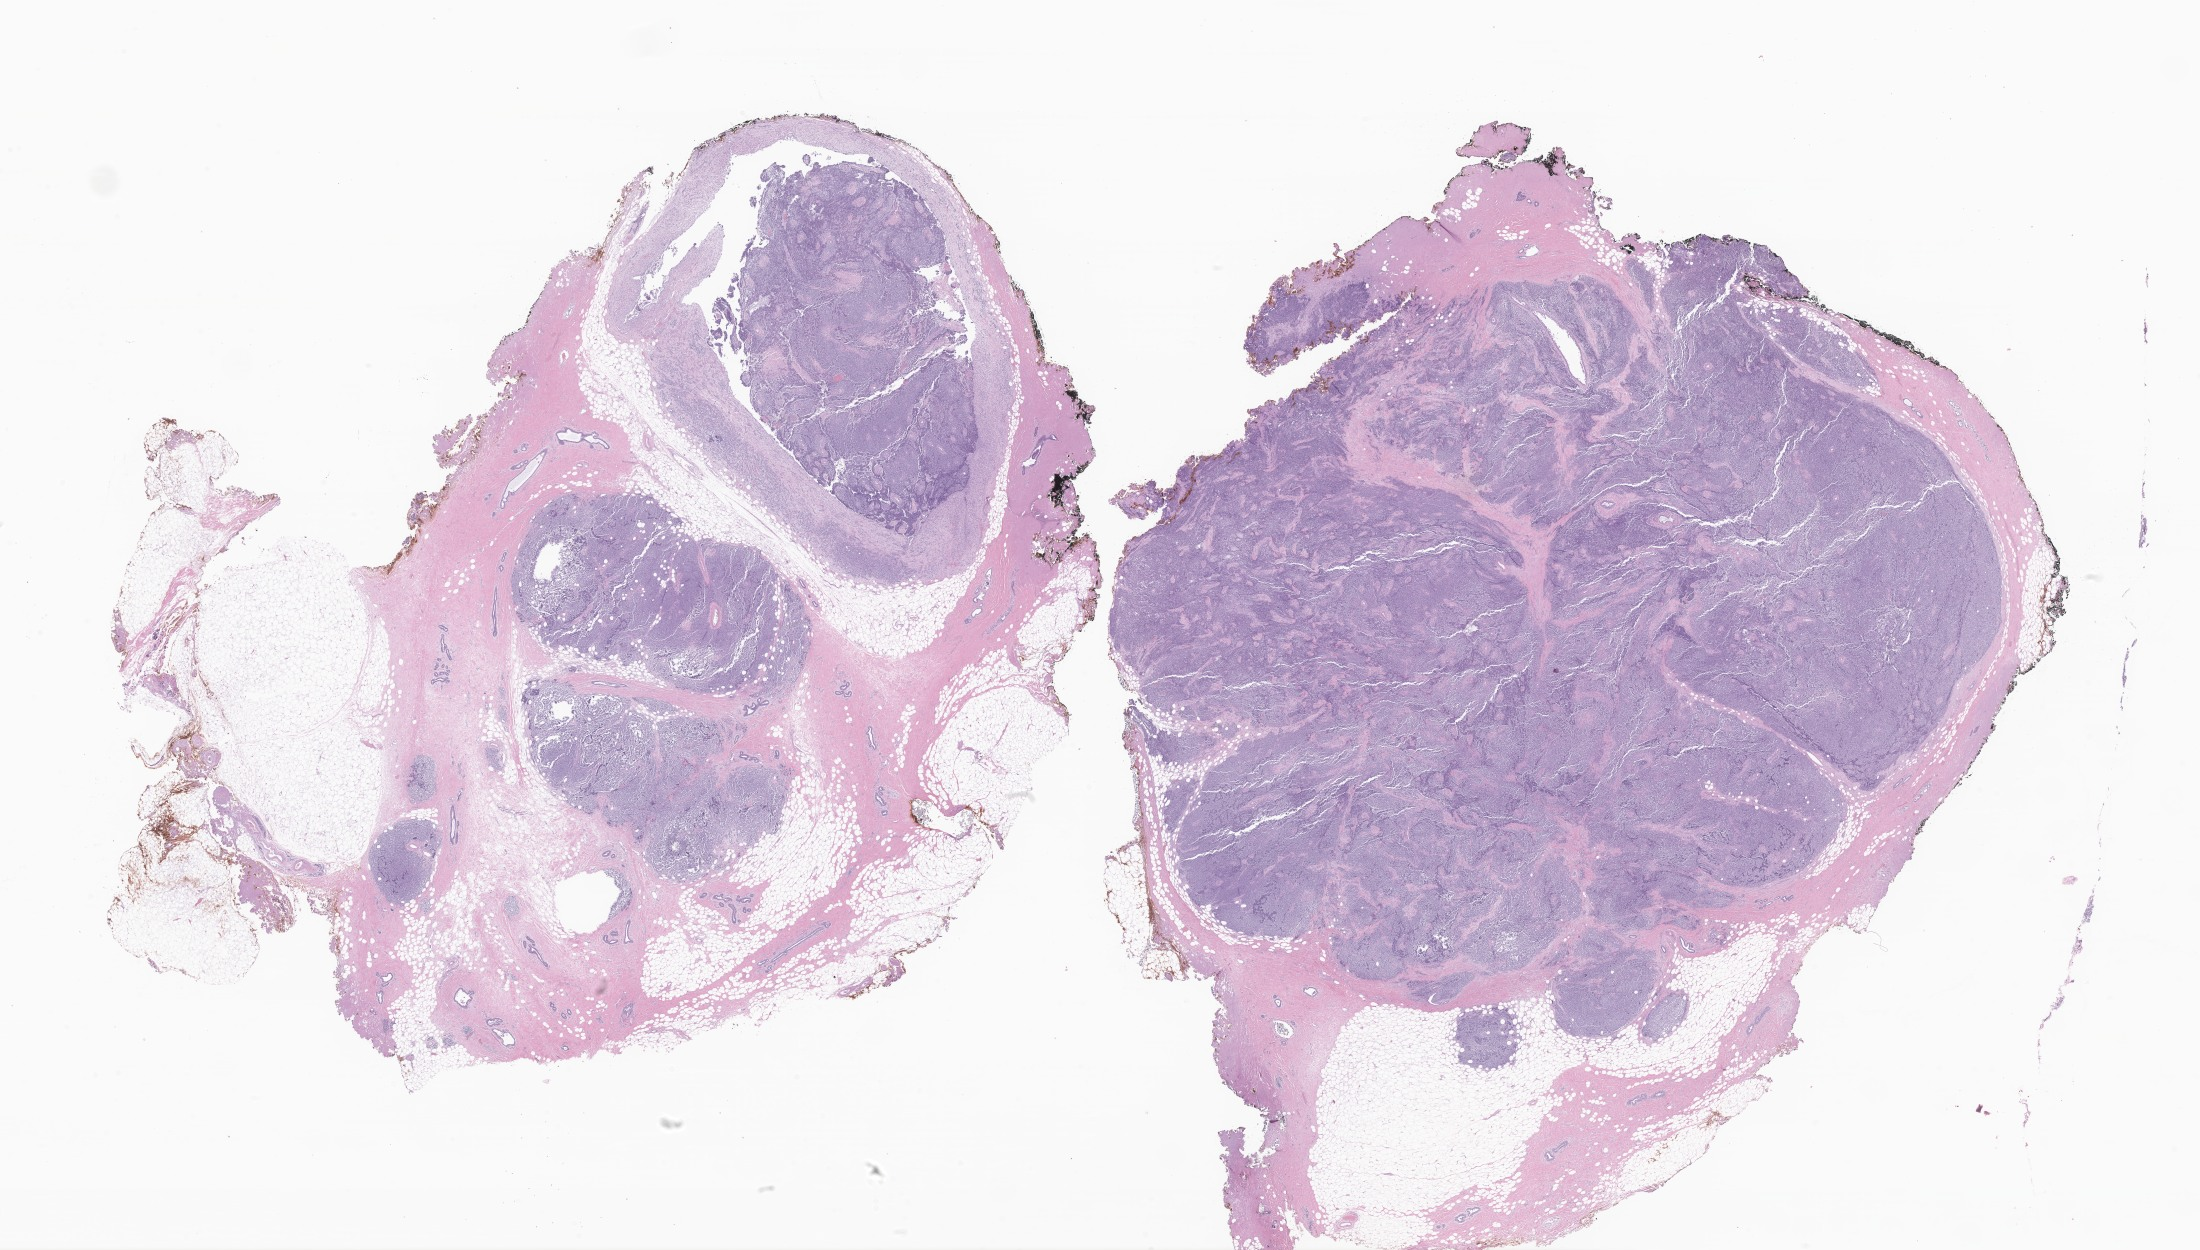
Whole-slide image, hematoxylin and eosin (H&E) stain of tumor tissue from the soft tissues of head and neck, low-resolution overview of the scanned area, about 37.1 x 21.1 mm, FFPE section. Female patient, age 176 months (14 years 8 months).
* diagnosis: Rhabdomyosarcoma, NOS